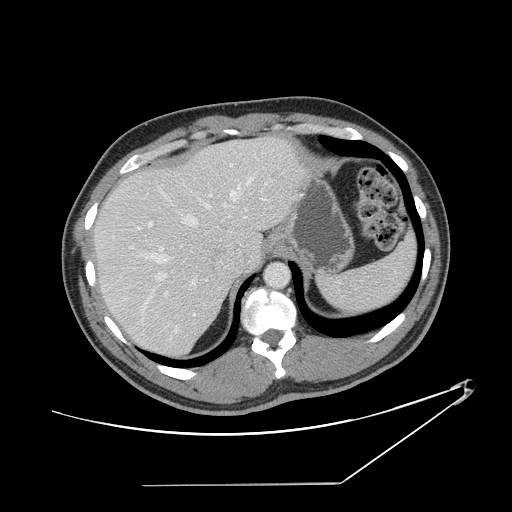
Contrast-enhanced abdominal CT, one axial slice; slice 112 of 152 in the series (ordered by position); intravenous contrast given; soft-tissue window (W 400 / L 40 HU); 512 × 512 image matrix, field of view 432 × 432 mm. Male patient, age 45 years. Case-level facts recorded for this patient, not image findings: diagnosis: colorectal cancer liver metastases, imaged before liver resection; multiple liver metastases: no; largest metastasis: 1 cm; disease in both lobes: no.
Annotated regions visible in this slice (expert manual segmentation):
- hepatic veins: bounding box (x1, y1, x2, y2) in pixels: (111, 173, 256, 312)
- liver: (95, 137, 302, 357)
- planned liver remnant (the part of the liver to remain after resection): (95, 159, 234, 358)
- portal vein (with intrahepatic branches): (159, 194, 265, 317)